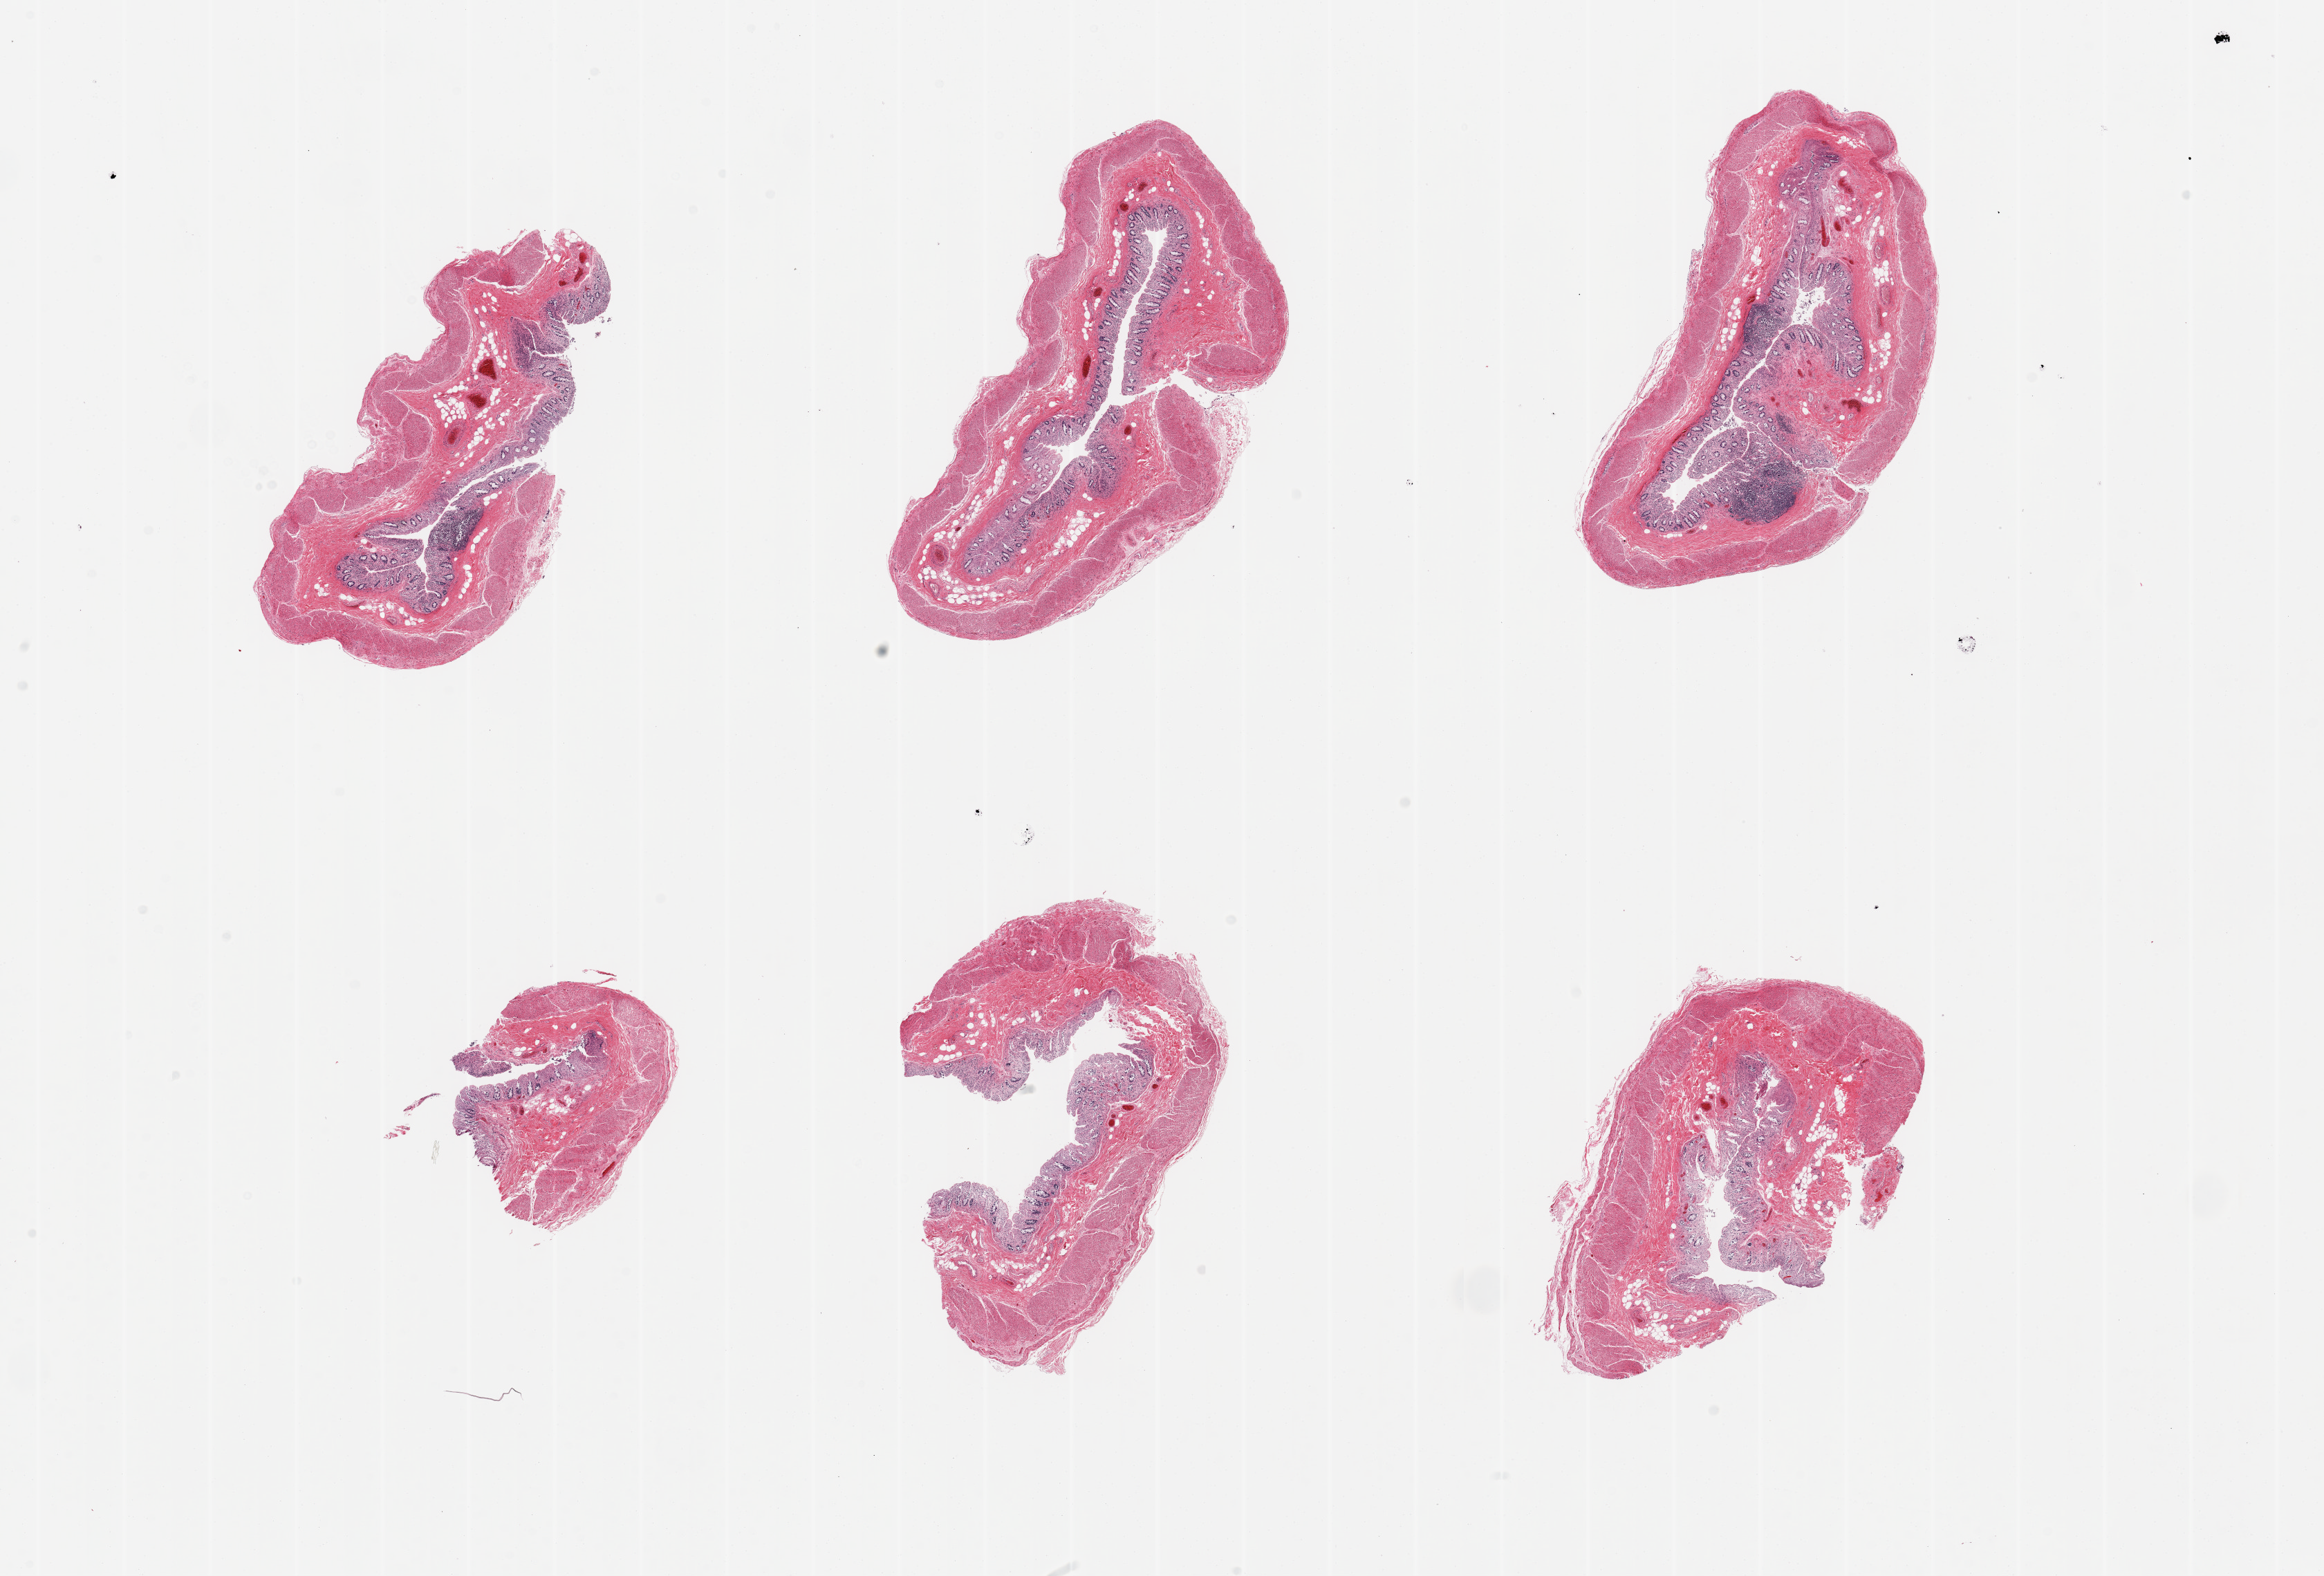
Whole-slide image, haematoxylin and eosin stain, brightfield, a low-resolution overview of the entire scanned area, about 26.6 x 18.0 mm, PAXgene-fixed paraffin-embedded (PFPE) section, target tissue: transverse colon, tissue donor sample. Male donor.
Reviewer comment on this tissue sample: 6 pieces, mucusa is badly autolyzed glandular elements but ~0.2mm thick, ~20% thickness.